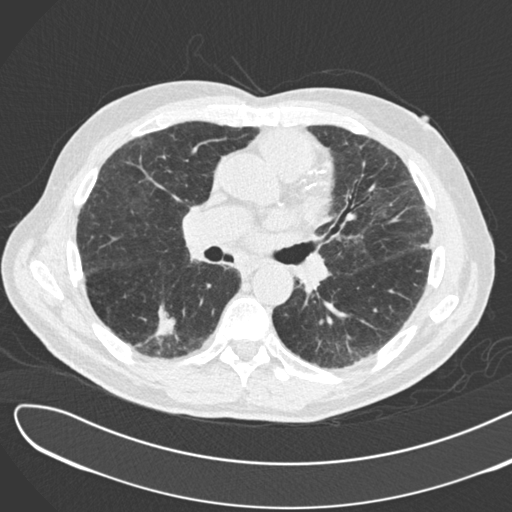
Chest CT (low-dose screening protocol), one axial image, second screening round (one year after baseline), lung window (W 1500 / L -600 HU), 120 kVp. Male, age 72 years at enrolment.
Expert-annotated lung lesion, bounding box (x1, y1, x2, y2) in pixels: (136, 292, 193, 347). The screening reader recorded 2 non-calcified nodules or masses ≥4 mm on this exam; which of them this box marks is not recorded. Official screen result: positive, change unspecified: nodule(s) >= 4 mm or enlarging nodule(s), mass(es), or other non-specific abnormalities suspicious for lung cancer.